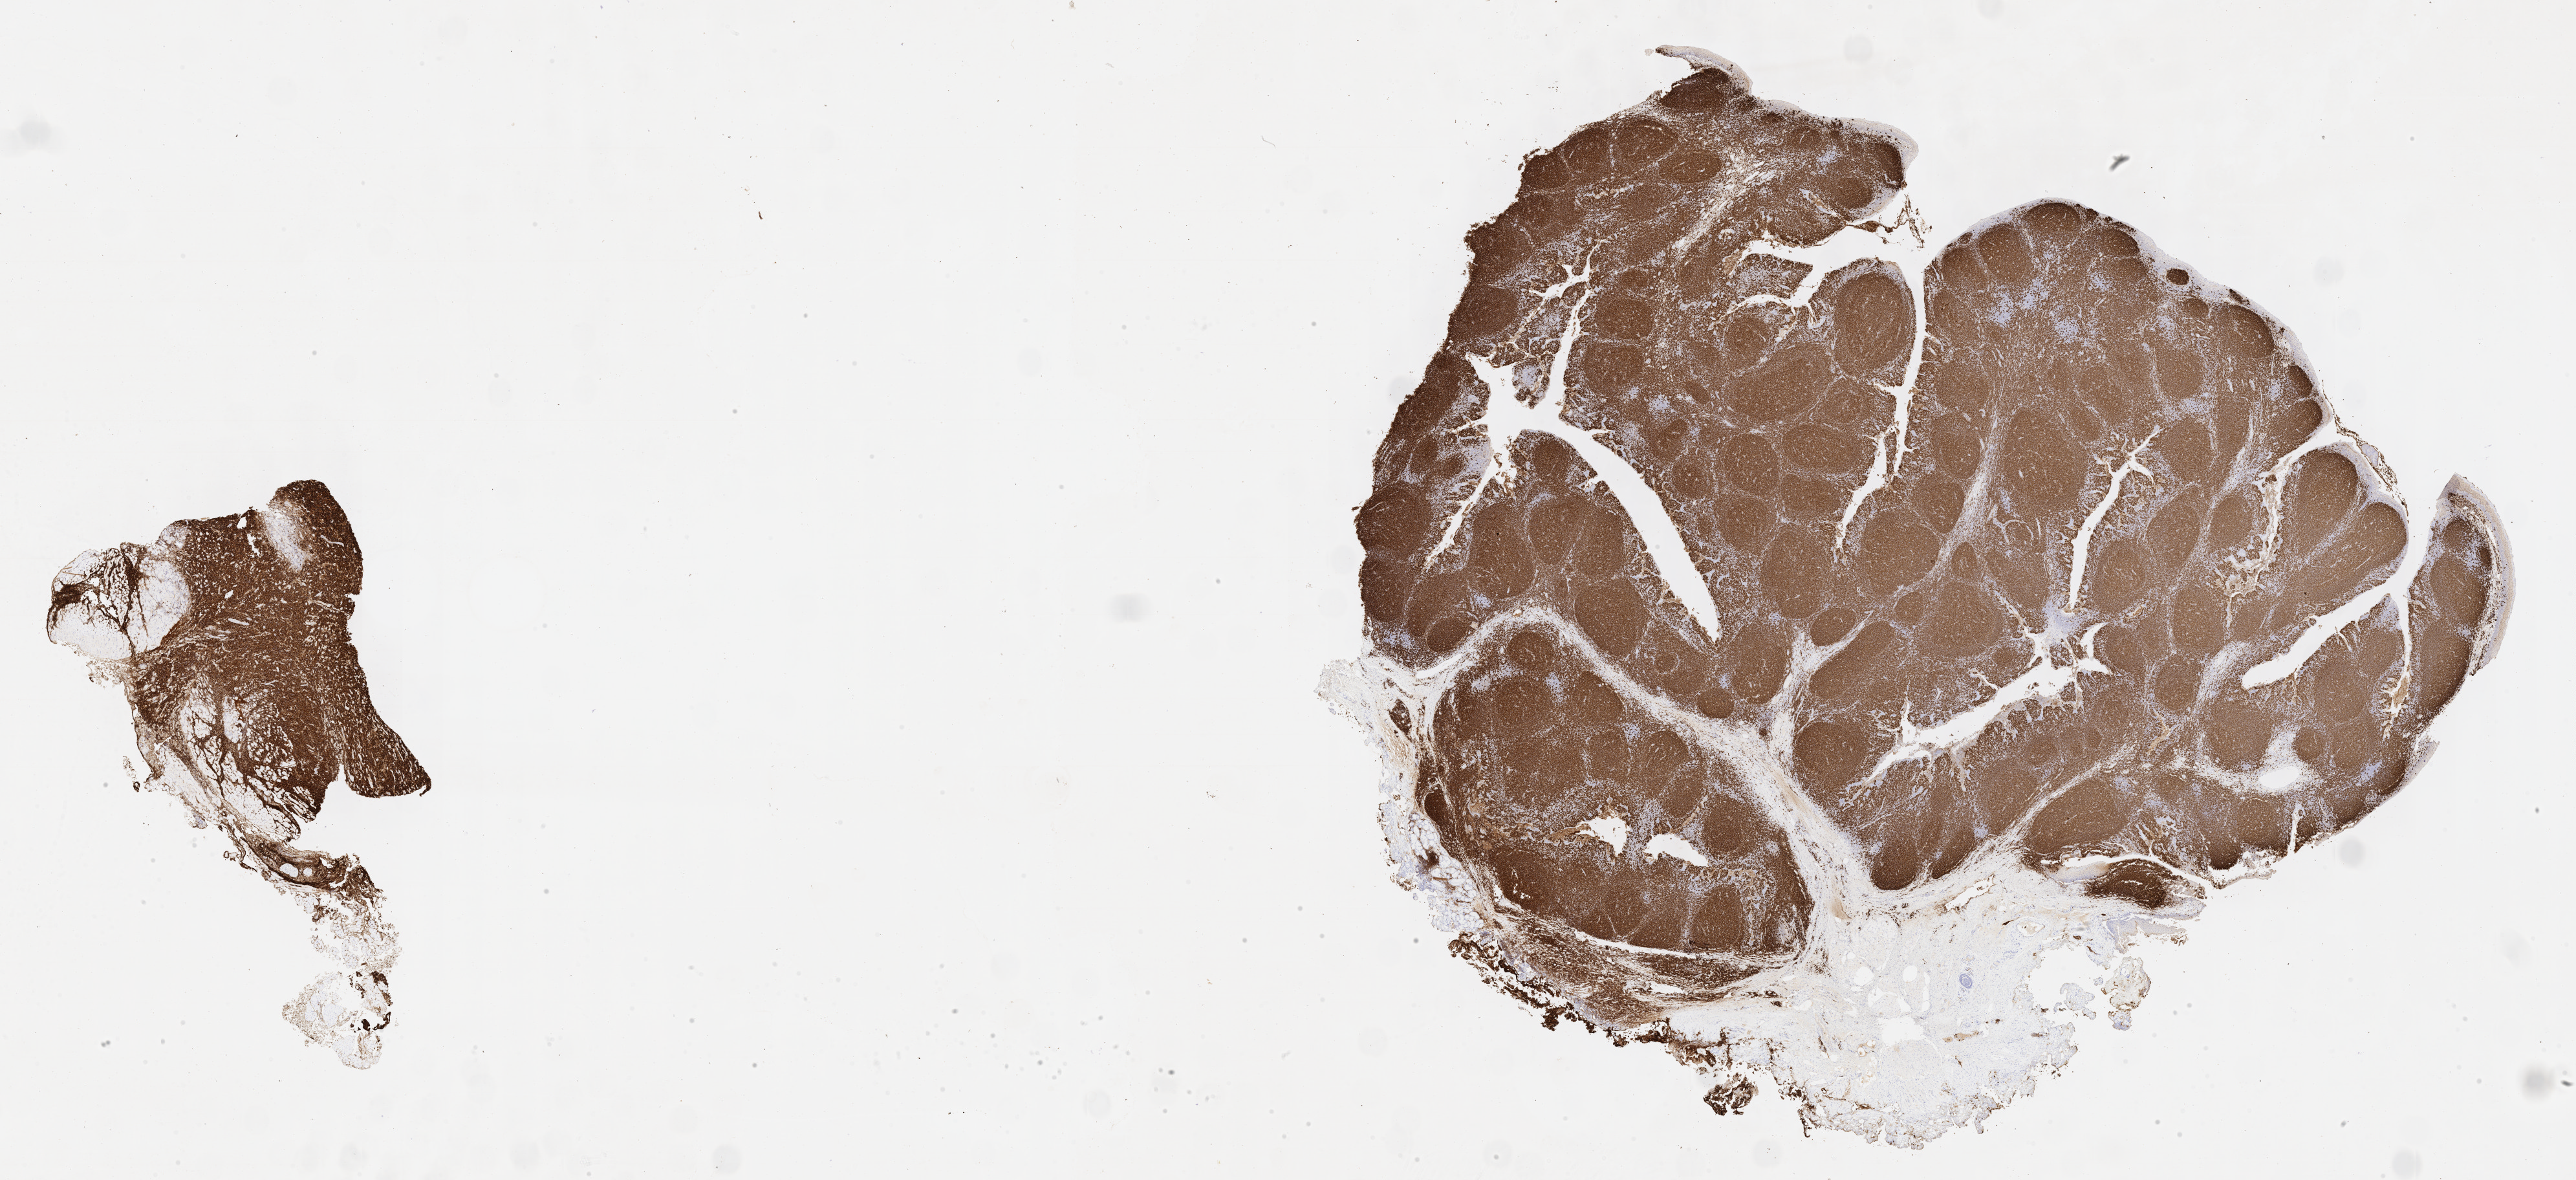
Whole-slide image, immunohistochemical stain for CD20, a low-resolution overview of the entire scanned area, about 32.2 x 14.7 mm; tumor tissue; anatomic site: kidney. Male patient, age 12 years.
Histologic diagnosis: Diffuse large B-cell lymphoma, NOS.